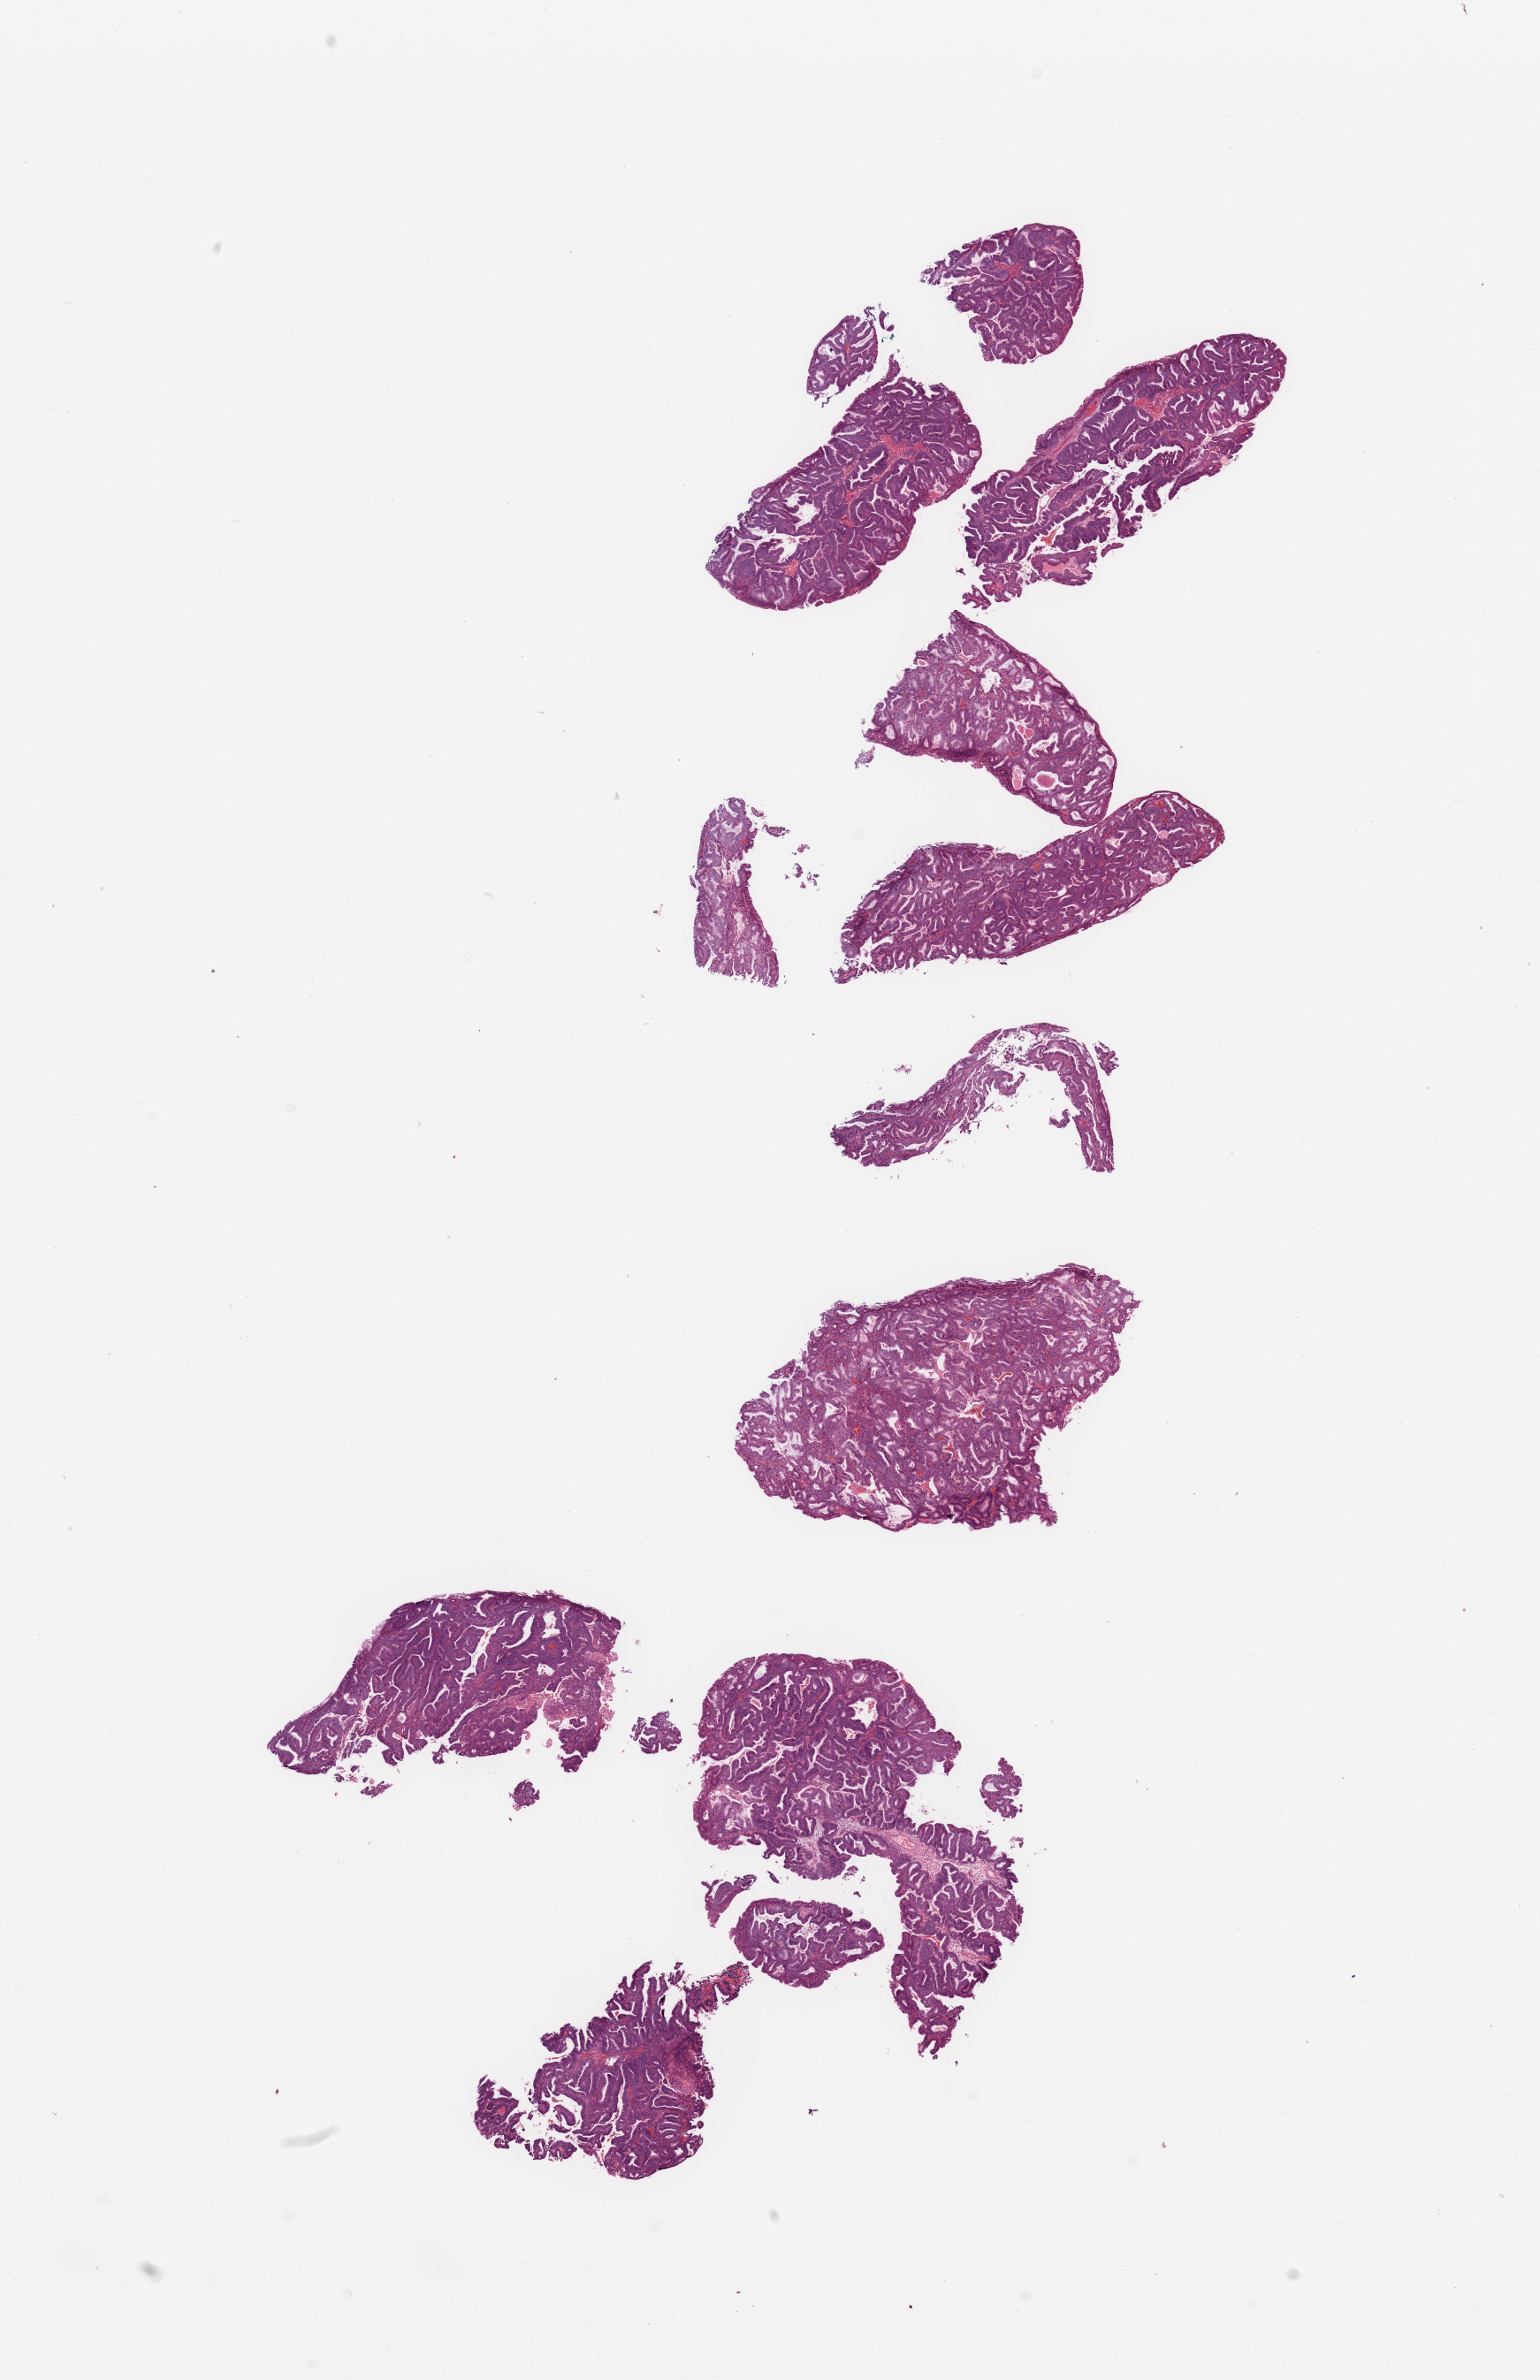
Digitized H&E-stained tissue section (whole slide), whole scanned area (about 13.8 x 21.3 mm, from a 20x scan) shown as a low-resolution overview. Tumour tissue sample, uterus. Female, 55 y/o.
Diagnosis: Endometrioid adenocarcinoma, NOS.